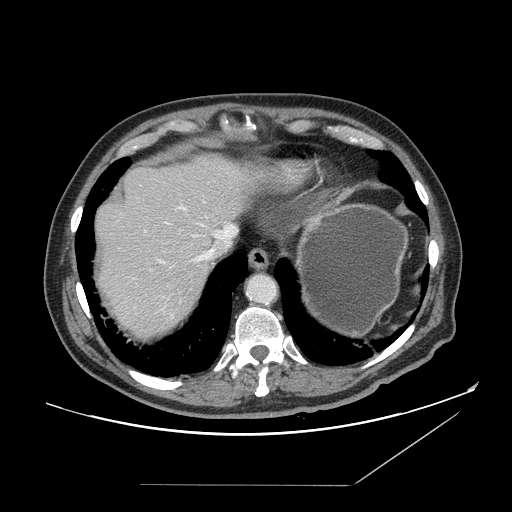
Contrast-enhanced abdominal CT, one axial slice. 120 kVp. Soft-tissue window (W 400 / L 40 HU). 512 × 512 image matrix. Male patient, age 80 years. Case-level facts recorded for this patient, not image findings: diagnosis: colorectal cancer liver metastases, imaged before liver resection; multiple liver metastases: no; largest metastasis: 2.2 cm; chemotherapy before resection: no.
Outlined on this slice (outlined manually by an expert reader):
- hepatic veins: bounding box <158,222,237,264> (left, top, right, bottom; pixels)
- liver: <94,153,255,339>
- planned liver remnant (the part of the liver to remain after resection): <94,154,256,258>
- portal vein (with intrahepatic branches): <182,208,187,211>